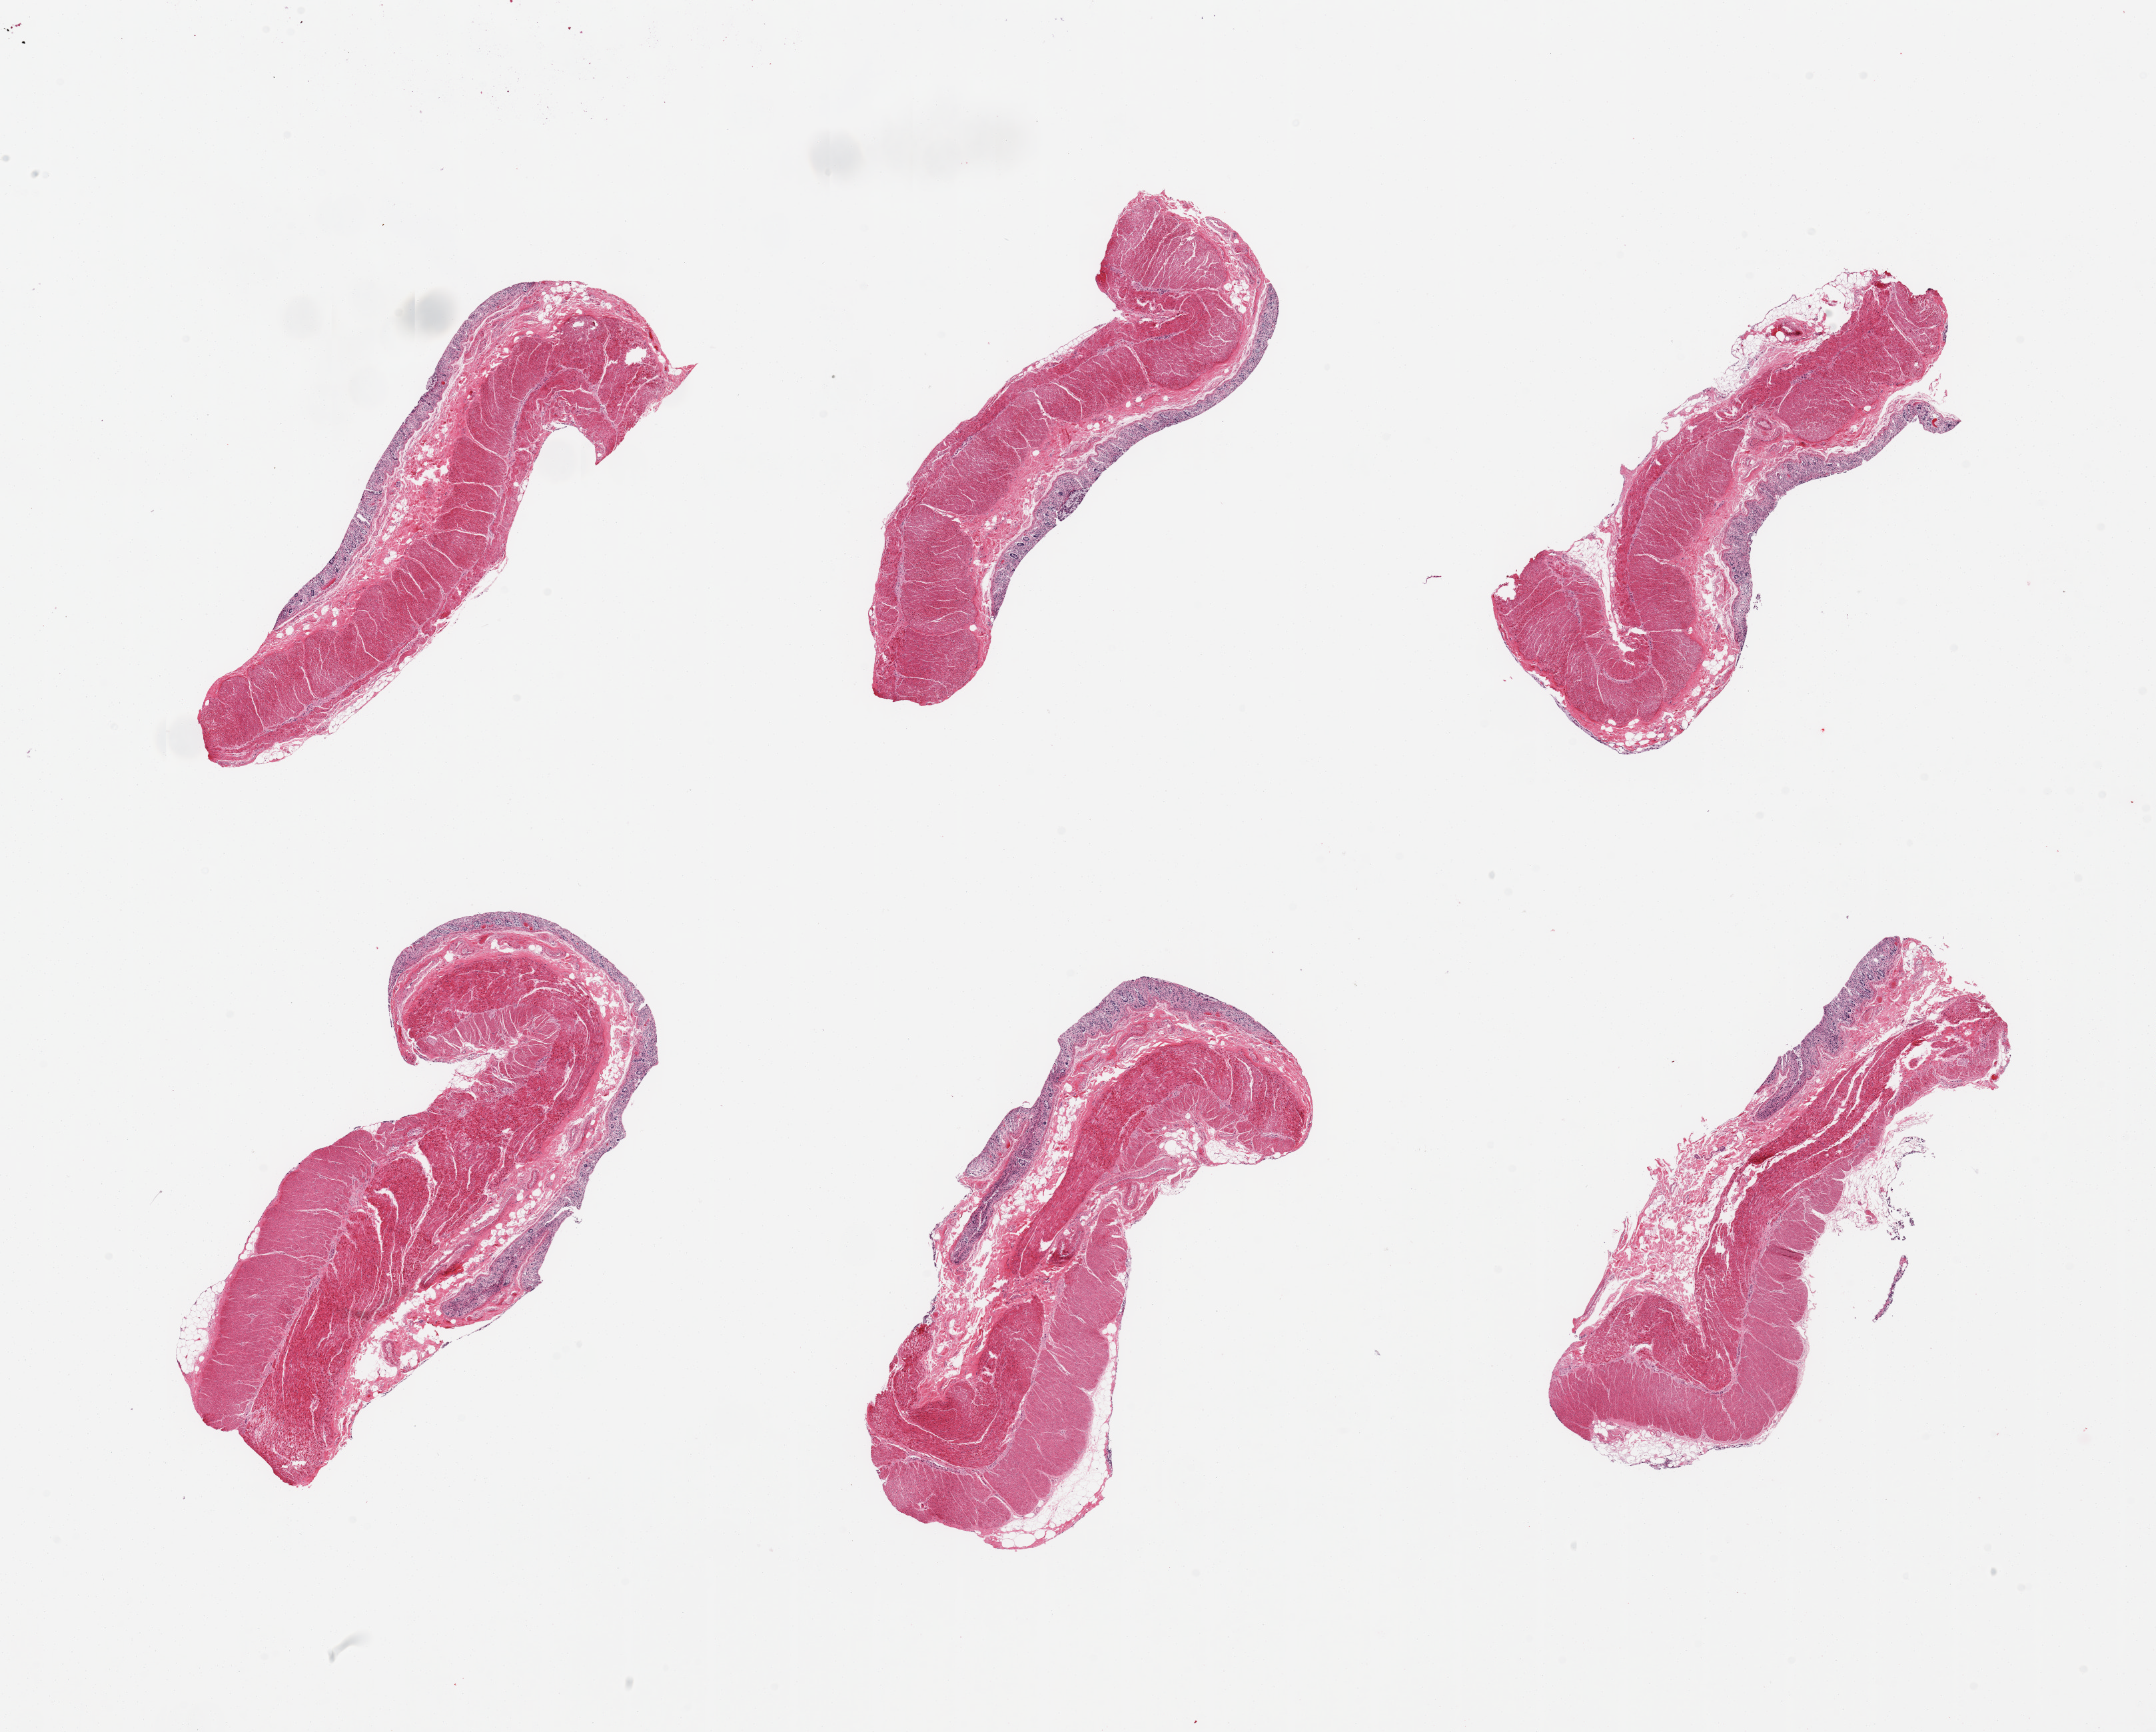
Whole-slide image, hematoxylin and eosin (H&E) stain, brightfield — low-resolution overview of the scanned area, about 25.6 x 20.6 mm (slide scanned at 20x). PAXgene-fixed, paraffin-embedded tissue. Section of transverse colon (target tissue). Tissue donor sample. Male donor.
Reviewer comment on this tissue sample: 6 pieces, mucosa up to ~0.3mm, advanced glandular autolysis.